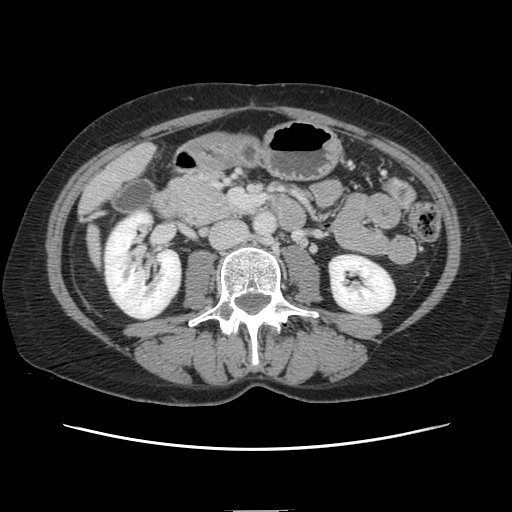
Contrast-enhanced abdominal CT, one axial slice. Slice 34 of 141 in the series (ordered by position). Intravenous contrast given. Soft-tissue window (W 400 / L 40 HU). 2.5 mm slice thickness. 512 × 512 image matrix, field of view 350 × 350 mm. Female patient, age 63 years. Case-level facts recorded for this patient, not image findings: diagnosis: colorectal cancer liver metastases, imaged before liver resection; multiple liver metastases: yes; largest metastasis: 3.2 cm; disease in both lobes: yes.
Outlined on this slice (outlined manually by an expert reader):
- liver: bounding box (x1, y1, x2, y2) in pixels: (83, 145, 154, 261)